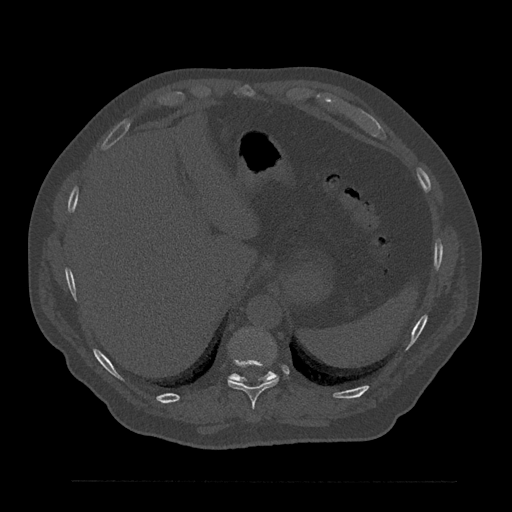
CT including the spine, one axial slice. Slice 331 of 797 in the series (ordered by position). 120 kVp. Bone window (W 1800 / L 400 HU). 0.5 mm slice thickness. 512 × 512 image matrix, field of view 430 × 430 mm. Male patient, age 61 years. Case-level facts recorded for this patient, not image findings: primary cancer: prostate.
Structures marked on this image (semi-automatic segmentation, software-assisted and operator-edited):
- T10 vertebra: bounding box [x1, y1, x2, y2] px = [227, 358, 279, 409]
- T11 vertebra: [229, 372, 277, 382]